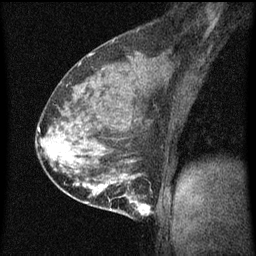
Breast MRI (dynamic contrast-enhanced), one sagittal slice; position 35 of 60 along the scan axis; dynamic contrast-enhanced series, image 2 of 3 at this slice position (ordered by acquisition); 1.5 T; TE 4.2 ms, TR 8 ms; 2 mm slice thickness; 256 × 256 image matrix, field of view 180 × 180 mm. Patient: female, 35 years.
Annotated regions visible in this slice (semi-automatically segmented with operator editing):
- analysis volume of interest (the breast-tissue region the enhancement analysis was run in; not a lesion): box from (x=110, y=178) to (x=155, y=219) px
- tumour enhancement mask (voxels above the 70 % enhancement threshold inside the analysis volume of interest): (x=110, y=178)–(x=152, y=215)